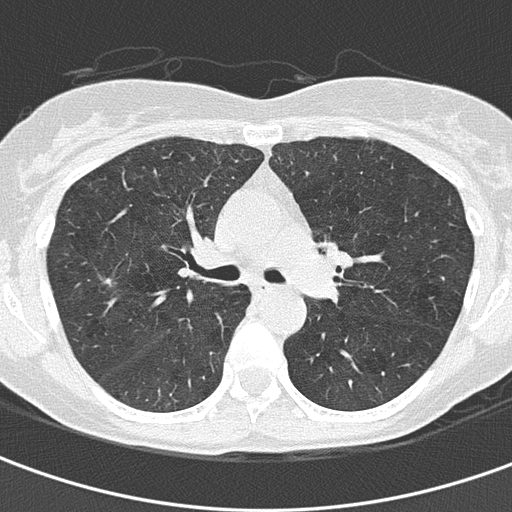
Axial slice from a low-dose chest CT screening exam. First (baseline) screen. Lung window (W 1500 / L -600 HU). 2 mm slice thickness. Slice 54 of 156 in the series. Female participant, aged 59 years at enrolment. Current smoker at enrolment.
• Lesion marked by an expert reader, box from (x=89, y=265) to (x=129, y=301) px.
• Screening reader's record for this exam: no non-calcified nodule ≥4 mm recorded.
• Official screen result: negative screen, minor abnormalities not suspicious for lung cancer.
• Later outcome: lung cancer diagnosed 834 days after this screen — bronchiolo-alveolar adenocarcinoma, NOS, right upper lobe, well differentiated (G1), stage IA (AJCC 6th edition), 4 mm at pathology.